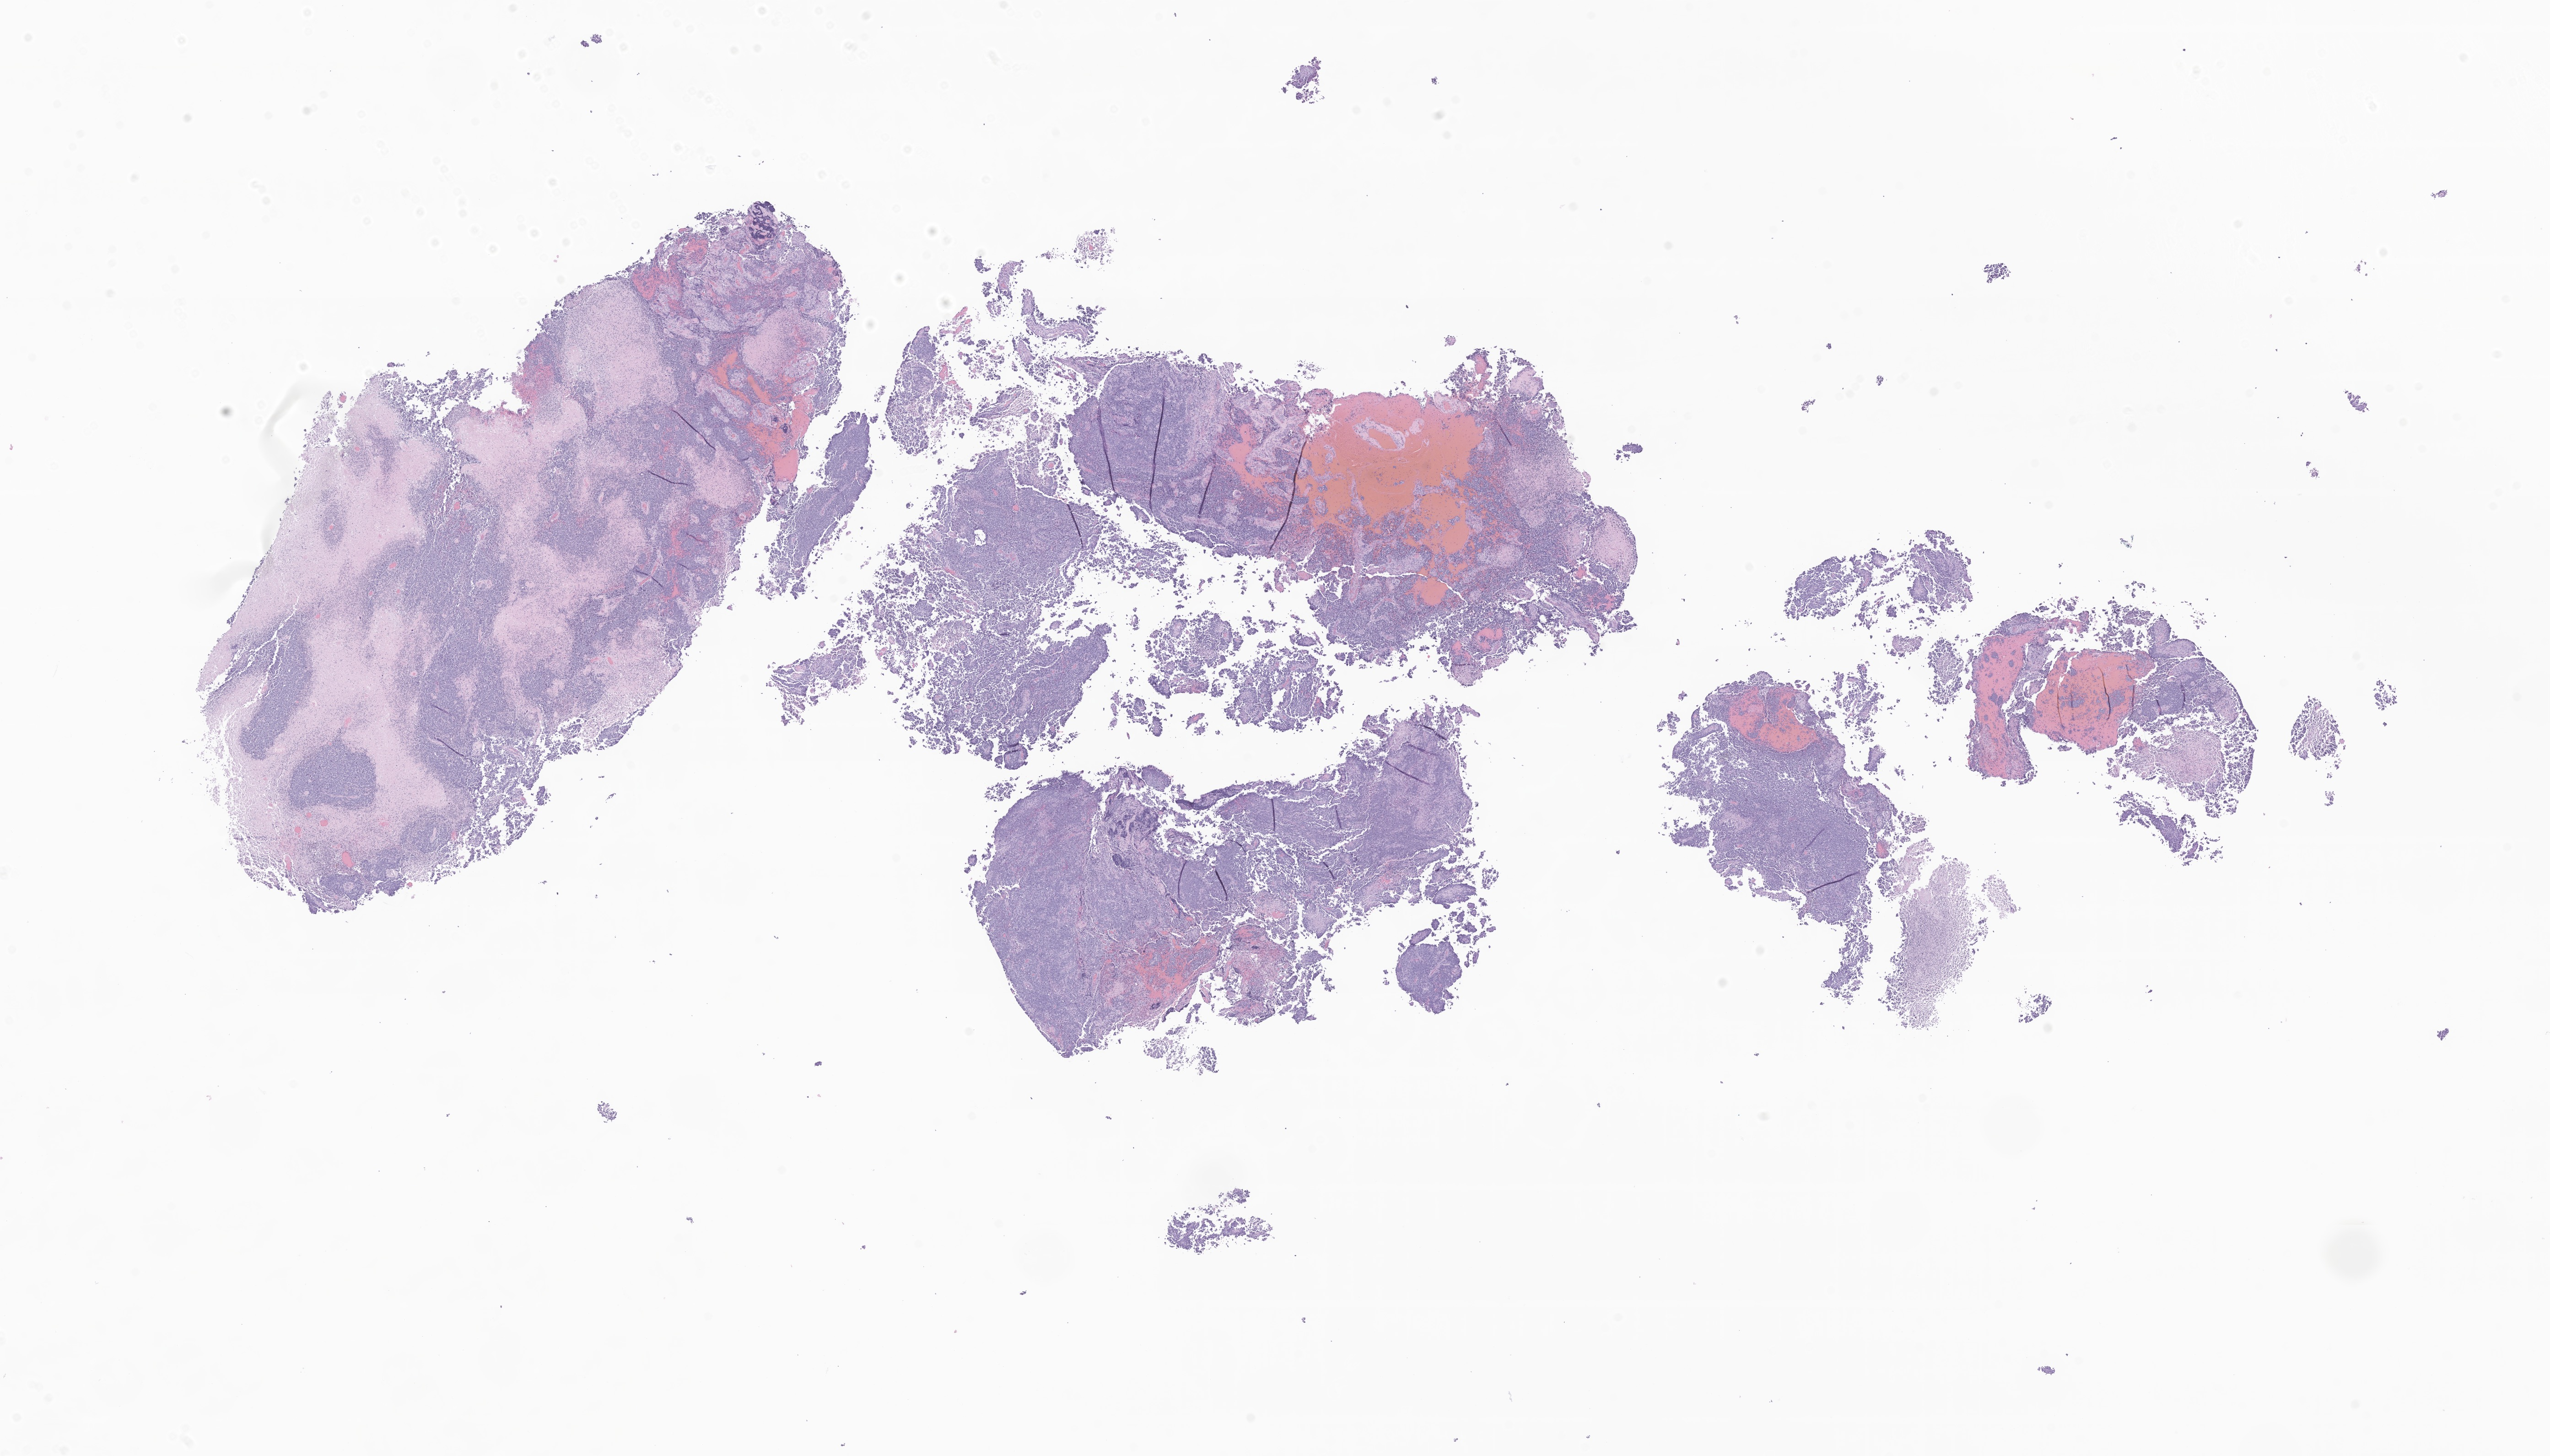
Digitized hematoxylin and eosin (H&E)-stained section of tumor tissue from the temporal lobe — a low-resolution overview of the entire scanned area, about 23.5 x 13.4 mm. Formalin-fixed paraffin-embedded section. Patient: female, age 167 months.
Diagnosis (ICD-O-3 morphology term): Neoplasm, malignant.